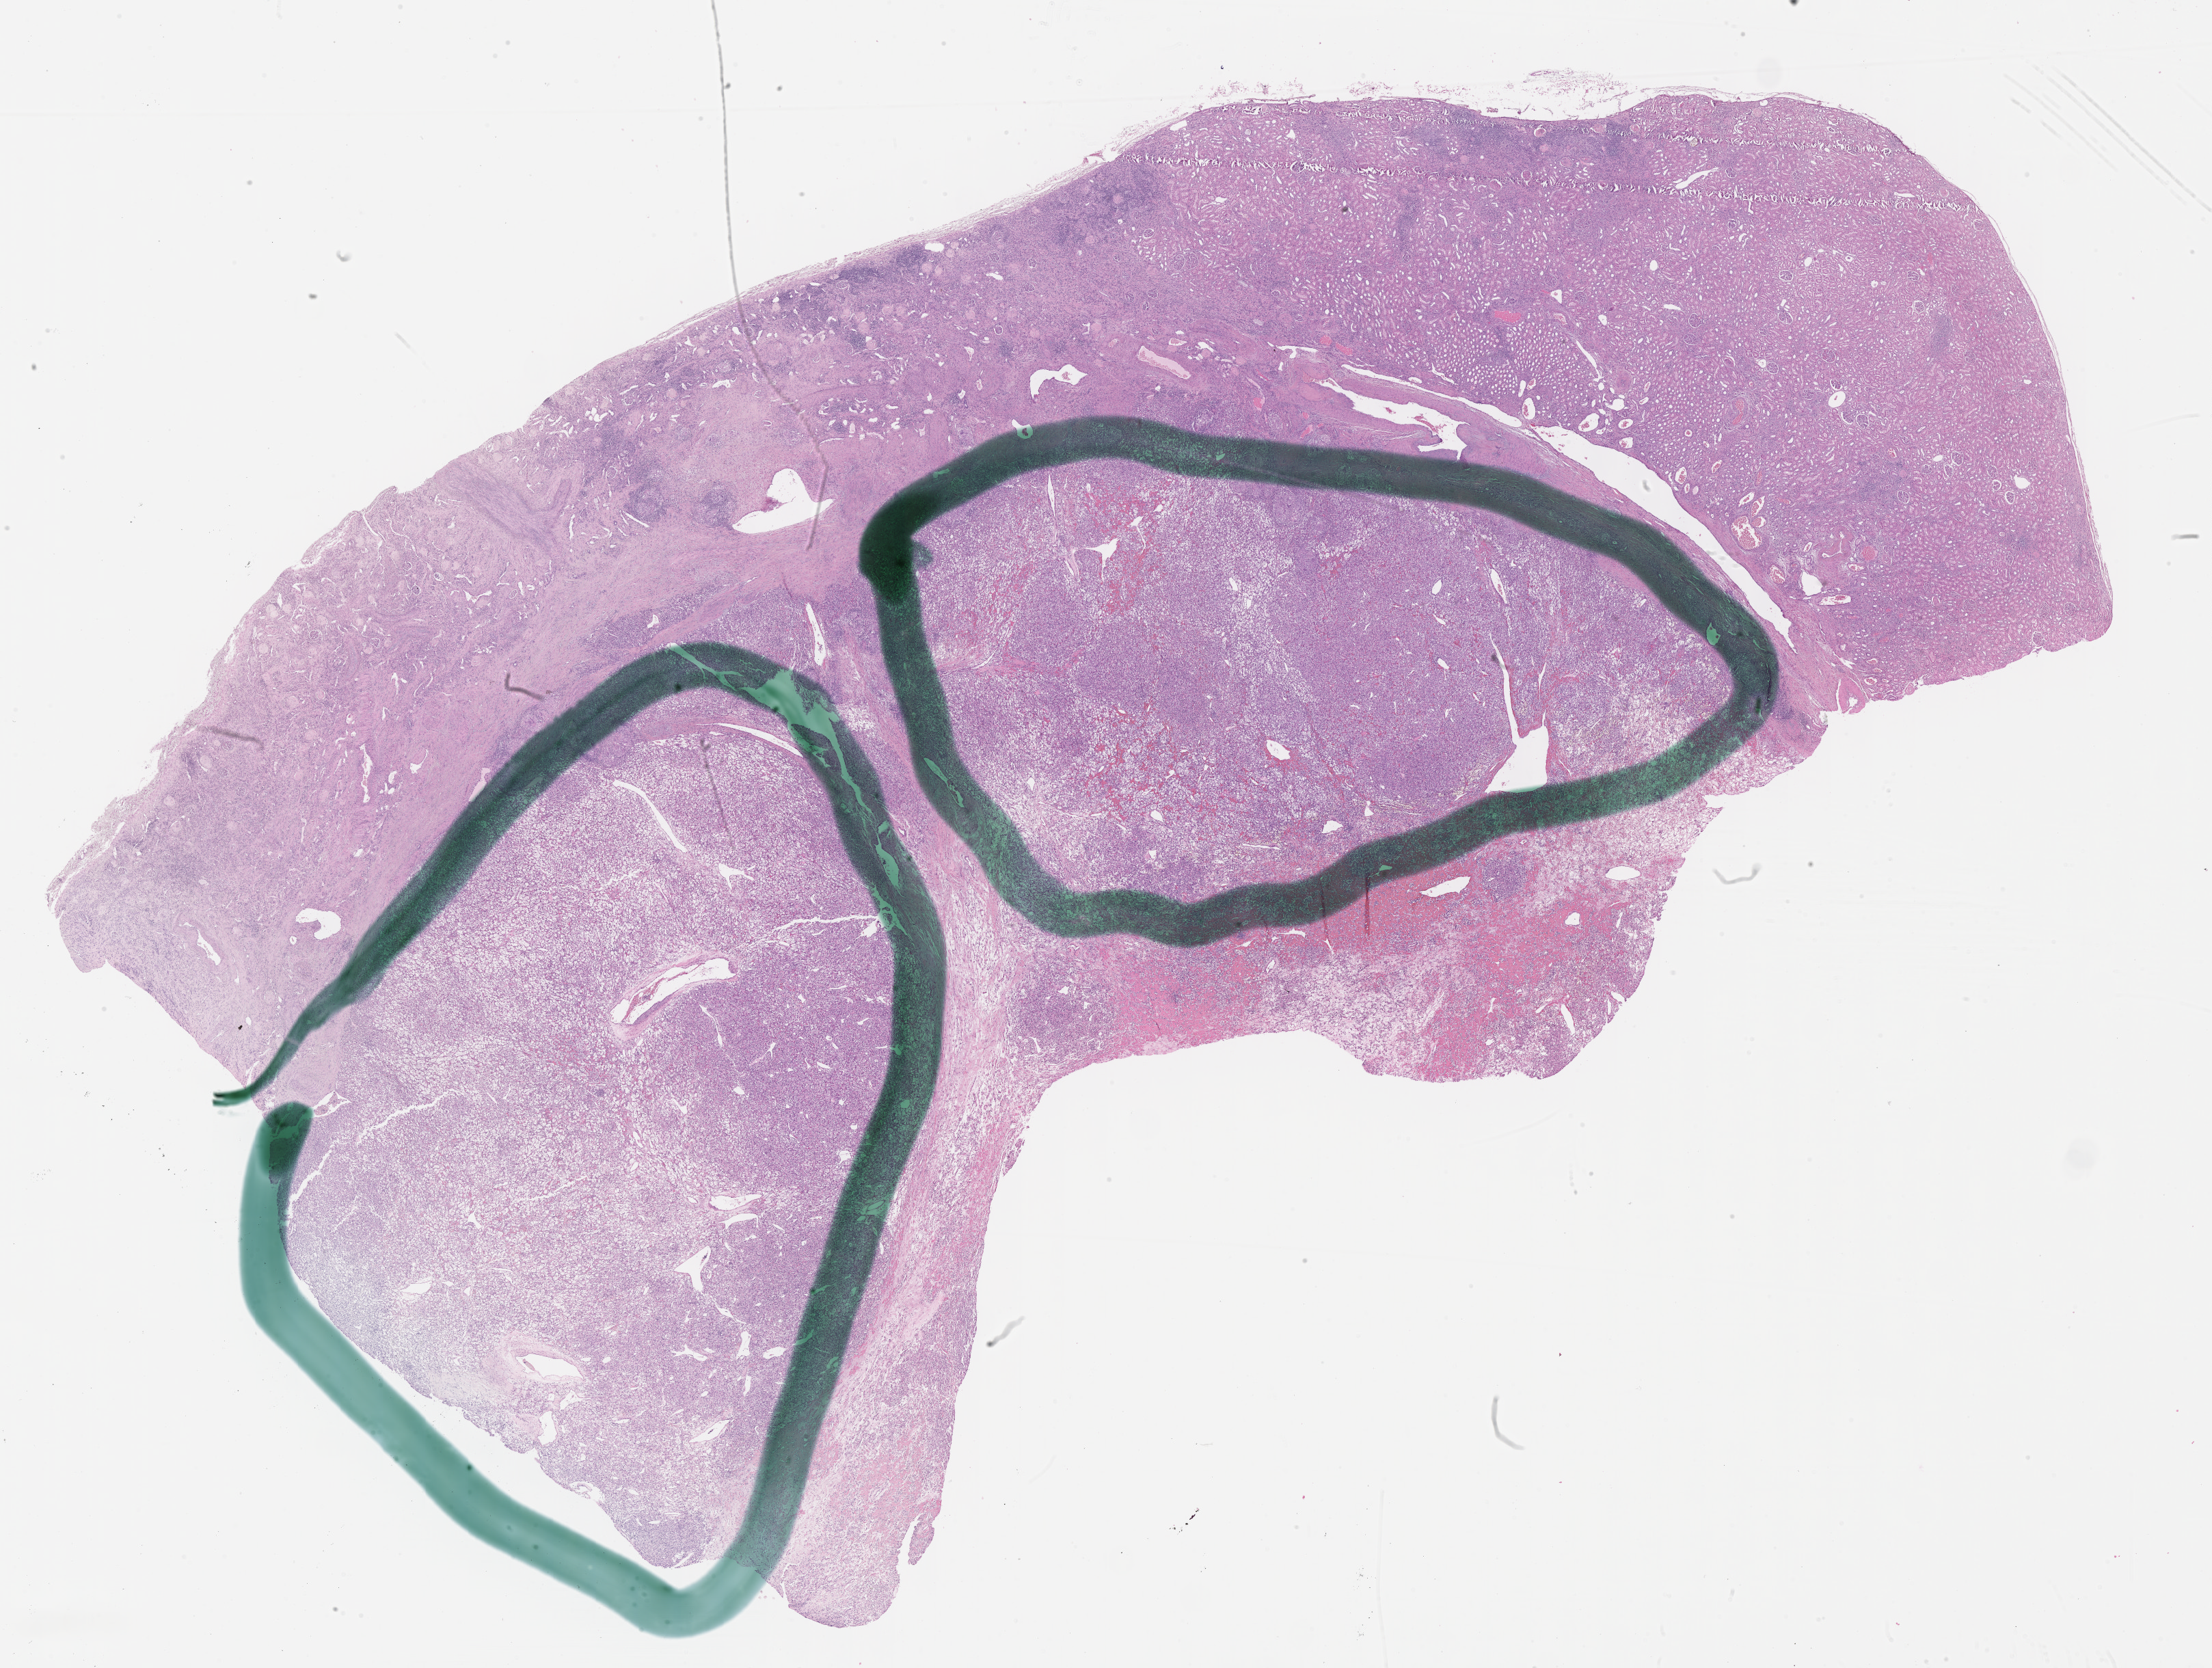
Whole-slide histology image, Hematoxylin and eosin (H&E) stained — whole scanned area (about 26.2 x 19.7 mm, slide scanned at 40x) shown as a low-resolution overview; FFPE section; primary tumour sample from the kidney. Patient: female, age at initial diagnosis 42 years. Histologic grade: G3 (poorly differentiated).
AJCC pathologic stage: I. Laterality: left. Diagnosis: Clear cell adenocarcinoma, NOS.